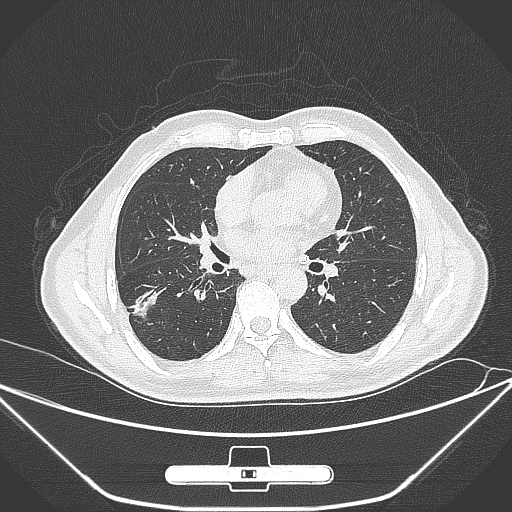
Chest CT, one axial slice; slice 145 of 310 in the series (ordered by position); 120 kVp; lung window (W 1500 / L -600 HU); 1 mm slice thickness; 512 × 512 image matrix, field of view 398 × 398 mm. Patient: male, 71 years. Case-level facts recorded for this patient, not image findings: clinical TNM (as recorded): T1c N0 M0.
Structures marked on this image (rectangle marked by the reading radiologist):
- lung tumour (recorded histology: adenocarcinoma): box from (x=127, y=280) to (x=166, y=336) px